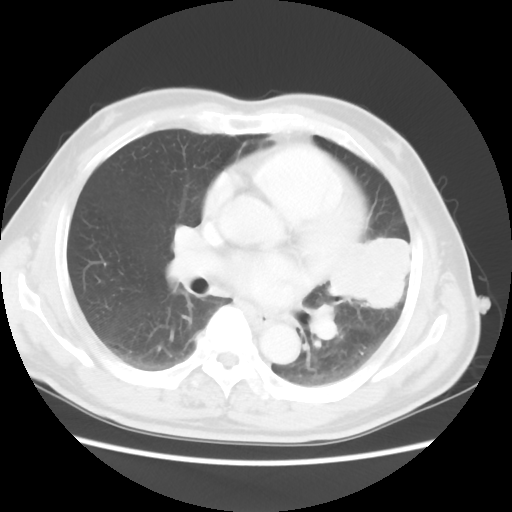
Chest CT, one axial slice. Slice 26 of 50 in the series (ordered by position). Reconstruction kernel STANDARD. Lung window (W 1500 / L -600 HU). 512 × 512 image matrix. Patient: male, 69 years. Case-level facts recorded for this patient, not image findings: clinical TNM (as recorded): T3 N1 M1a.
Outlined on this slice (bounding box drawn by a radiologist):
- lung tumour (recorded histology: squamous cell carcinoma): bounding box <328,228,419,318> (left, top, right, bottom; pixels)